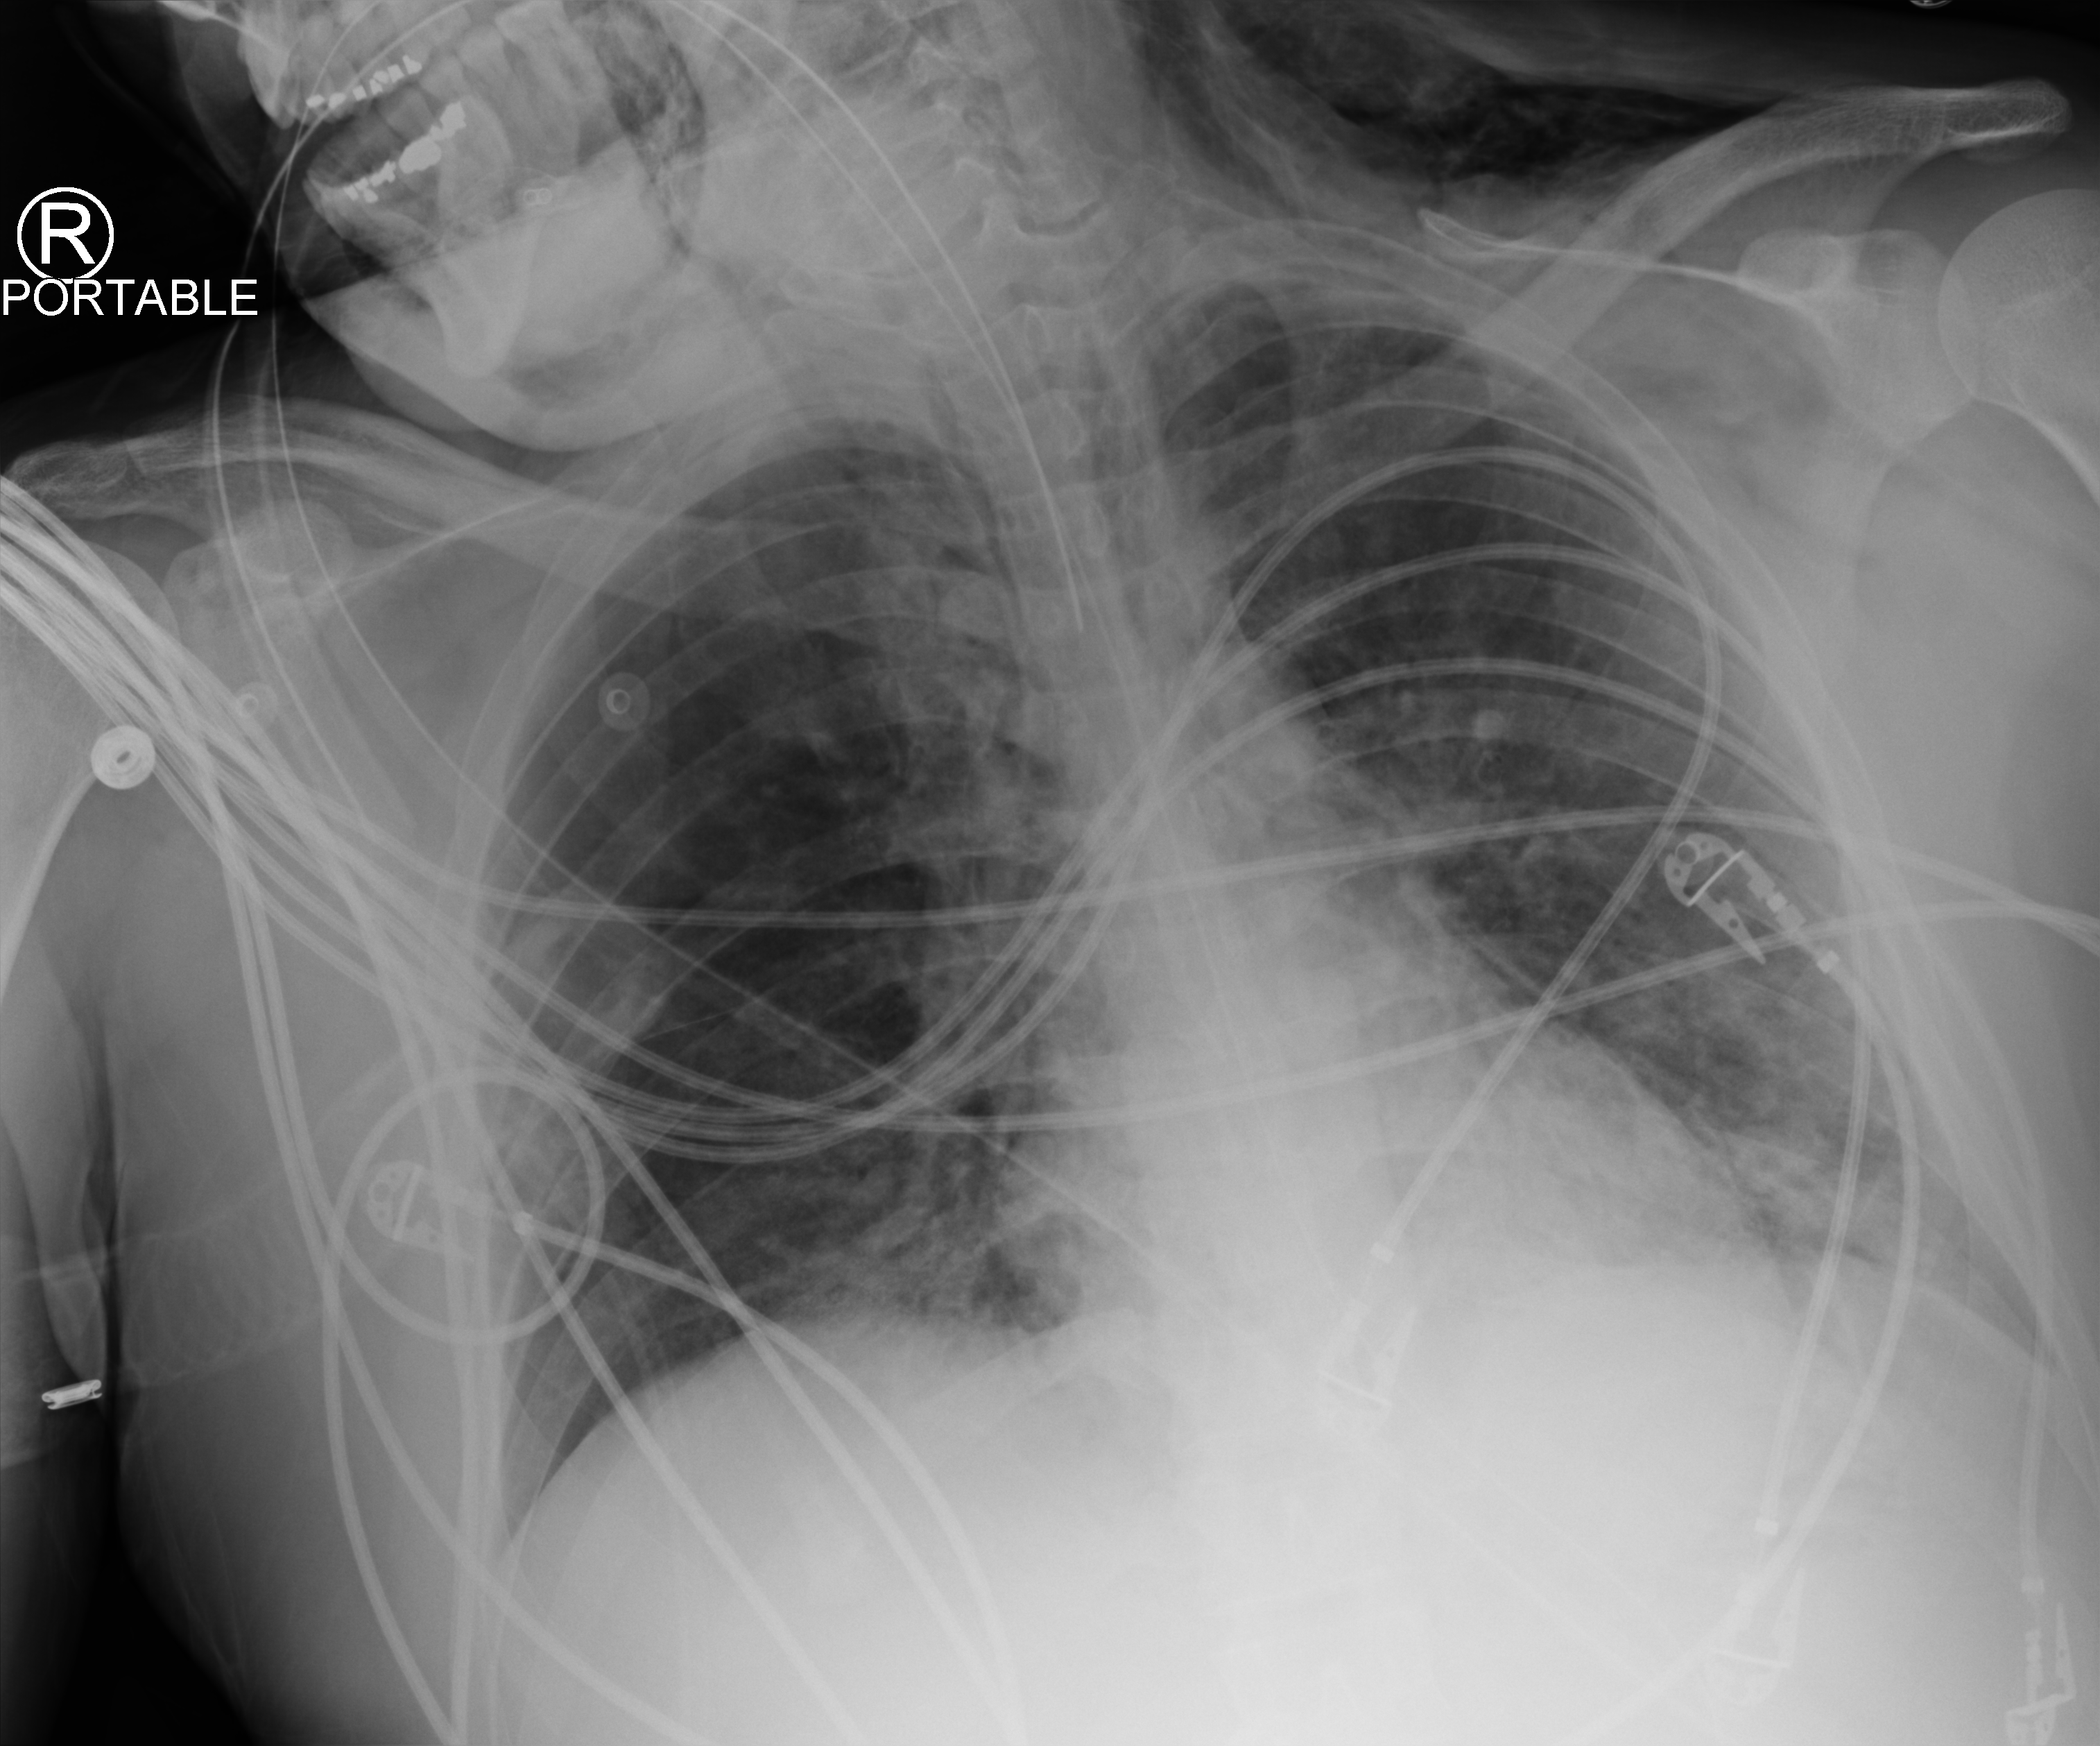
Chest X-ray (portable), anteroposterior (AP) projection. Adult patient hospitalised with COVID-19, age 18–59 years.
From the hospital-stay record, not from the radiograph (when in the stay this image was taken is not recorded):
- mechanically ventilated during this hospital stay: yes
- admitted to intensive care during this hospital stay: yes